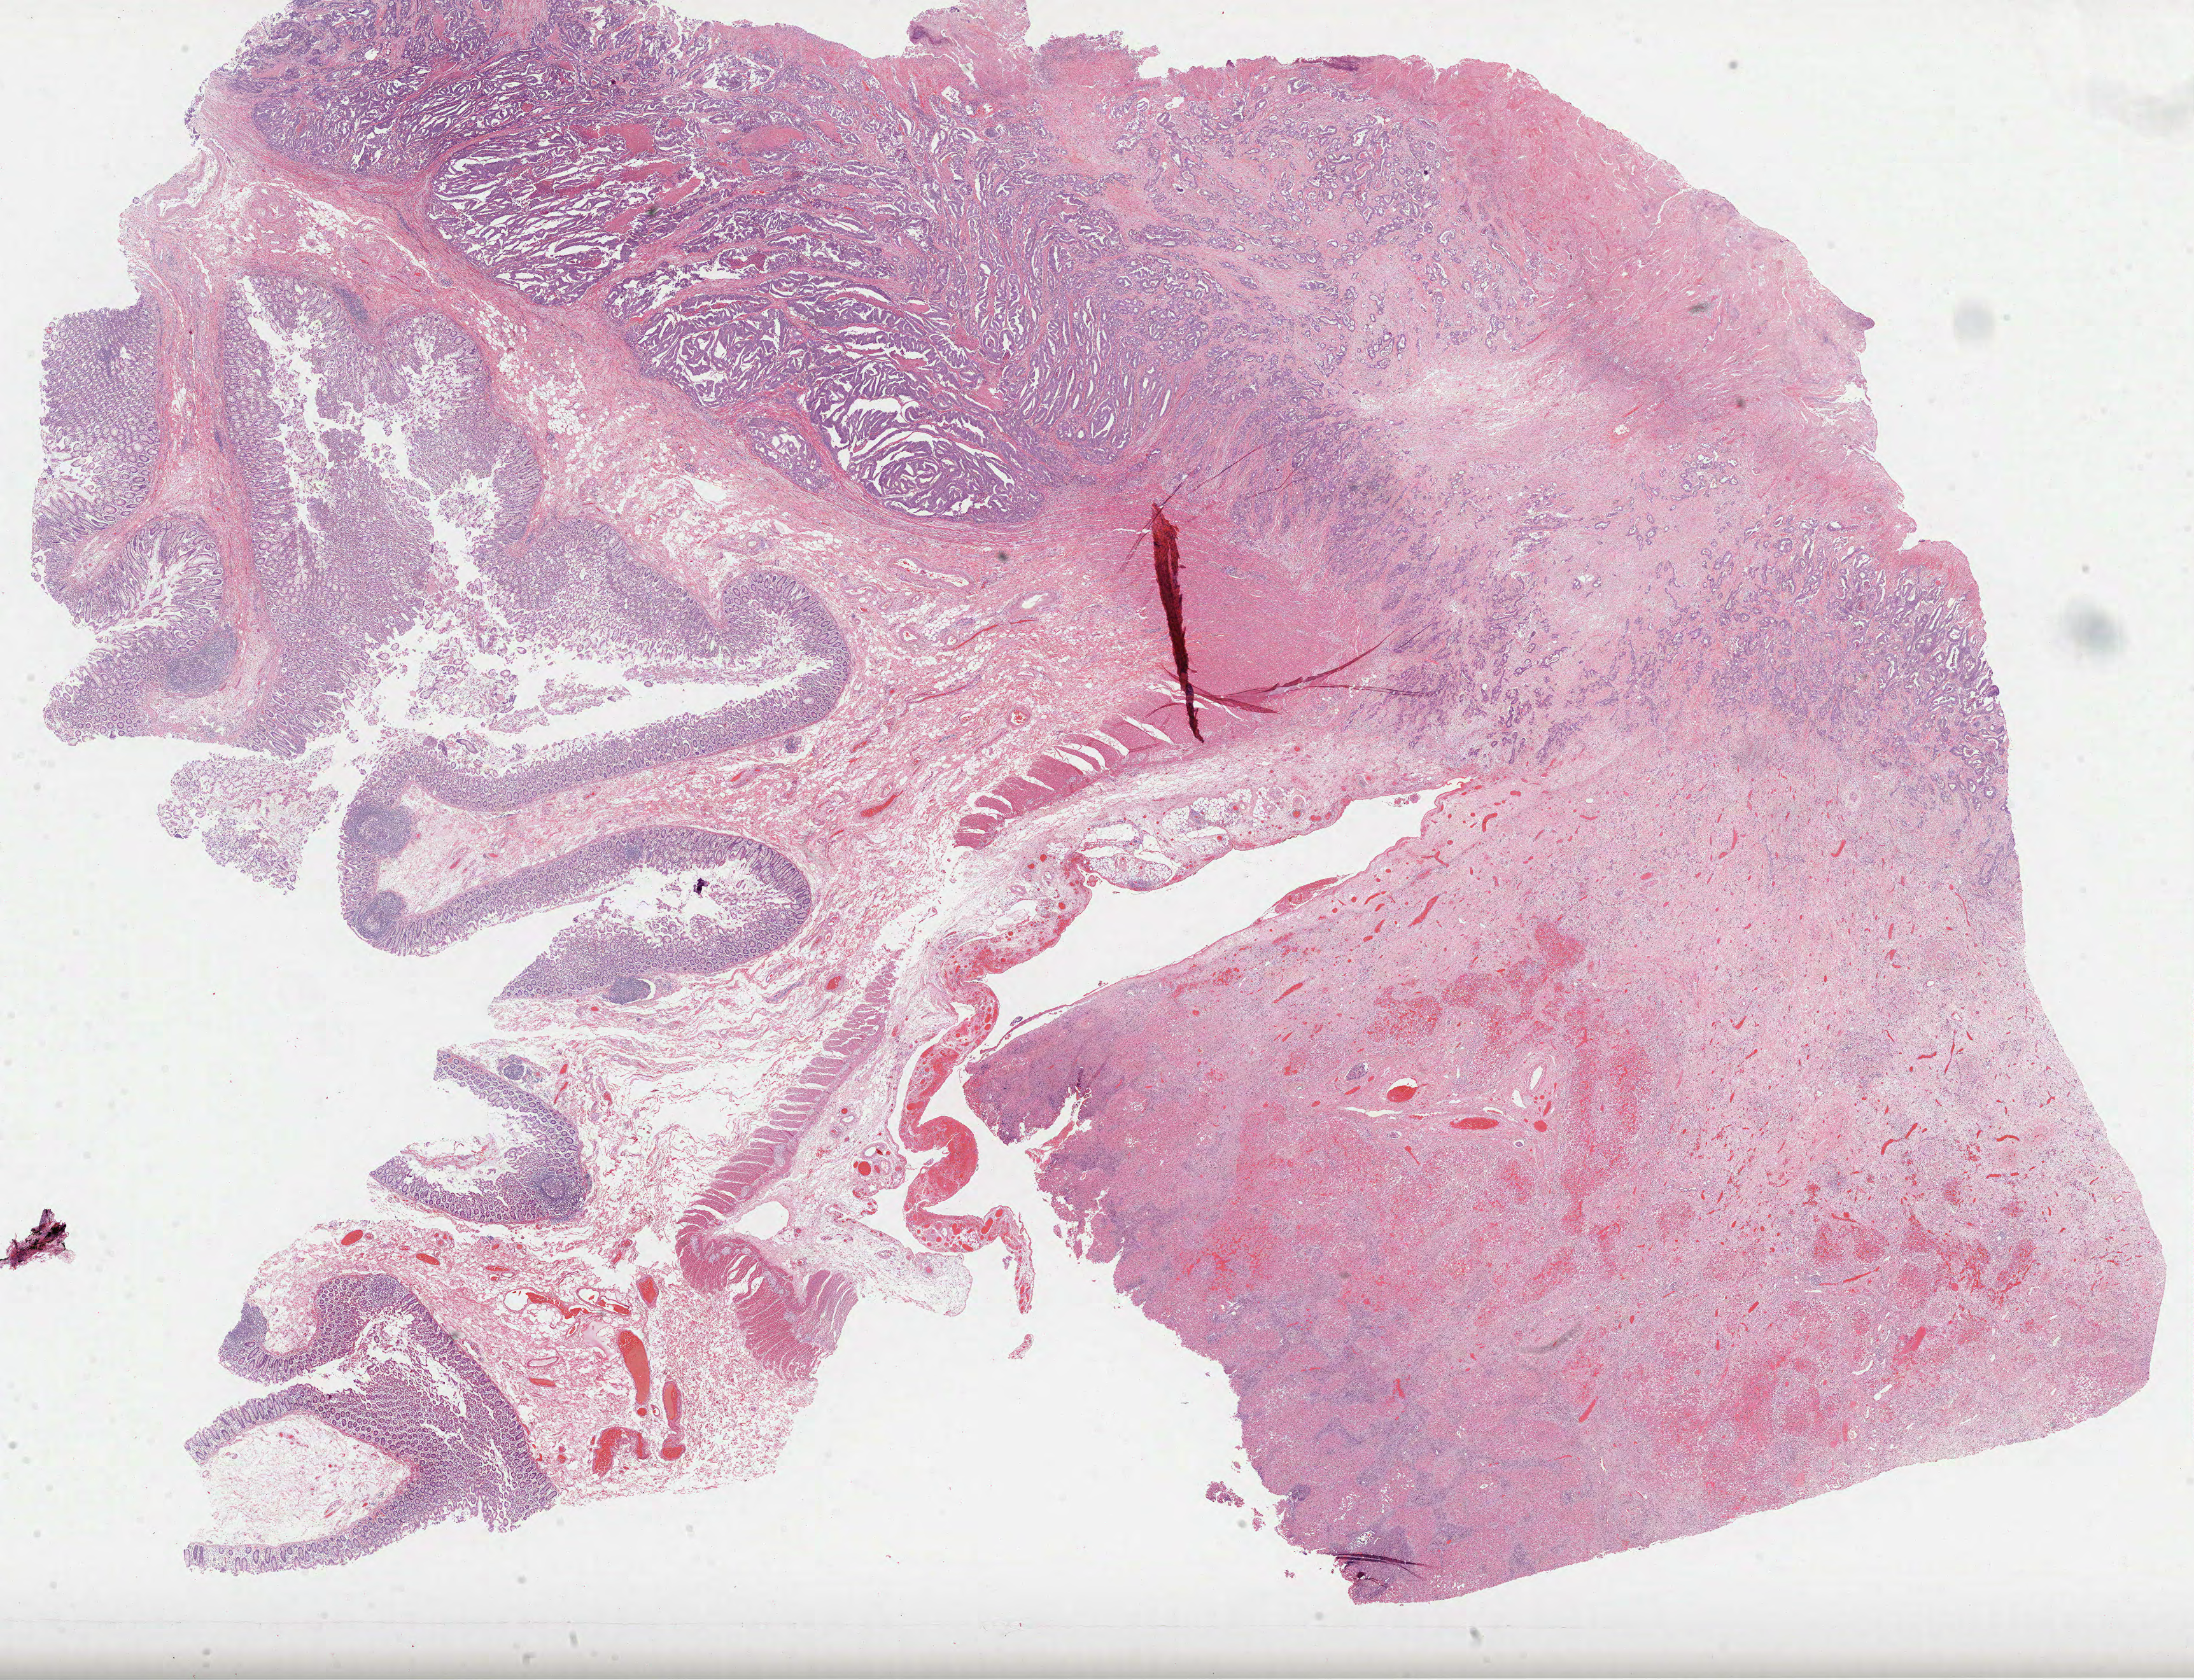
Digitized Hematoxylin and eosin (H&E) stained tissue section (whole slide) — low-resolution overview of the scanned area, about 27.8 x 21.3 mm; FFPE section; sample: primary tumour, colon. Male patient.
* lymph nodes positive (case pathology): 1 of 37 examined
* diagnosis: Adenocarcinoma, NOS (cecum)
* AJCC pathologic stage: IIIB (6th edition)